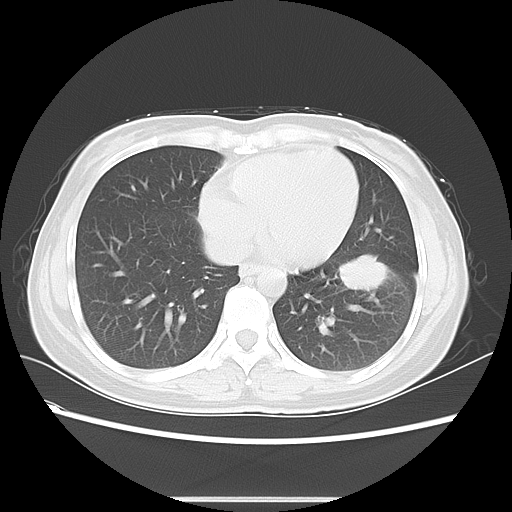
Chest CT, one axial slice; slice 22 of 55 in the series (ordered by position); reconstruction kernel LUNG; 120 kVp; lung window (W 1500 / L -600 HU); 512 × 512 image matrix, field of view 350 × 350 mm. Patient: female, 41 years. From the clinical record (not read from this slice): clinical TNM (as recorded): T1c N3 M1b.
Structures marked on this image (bounding box drawn by a radiologist):
- lung tumour (recorded histology: adenocarcinoma): bounding box (x1, y1, x2, y2) in pixels: (332, 245, 394, 303)